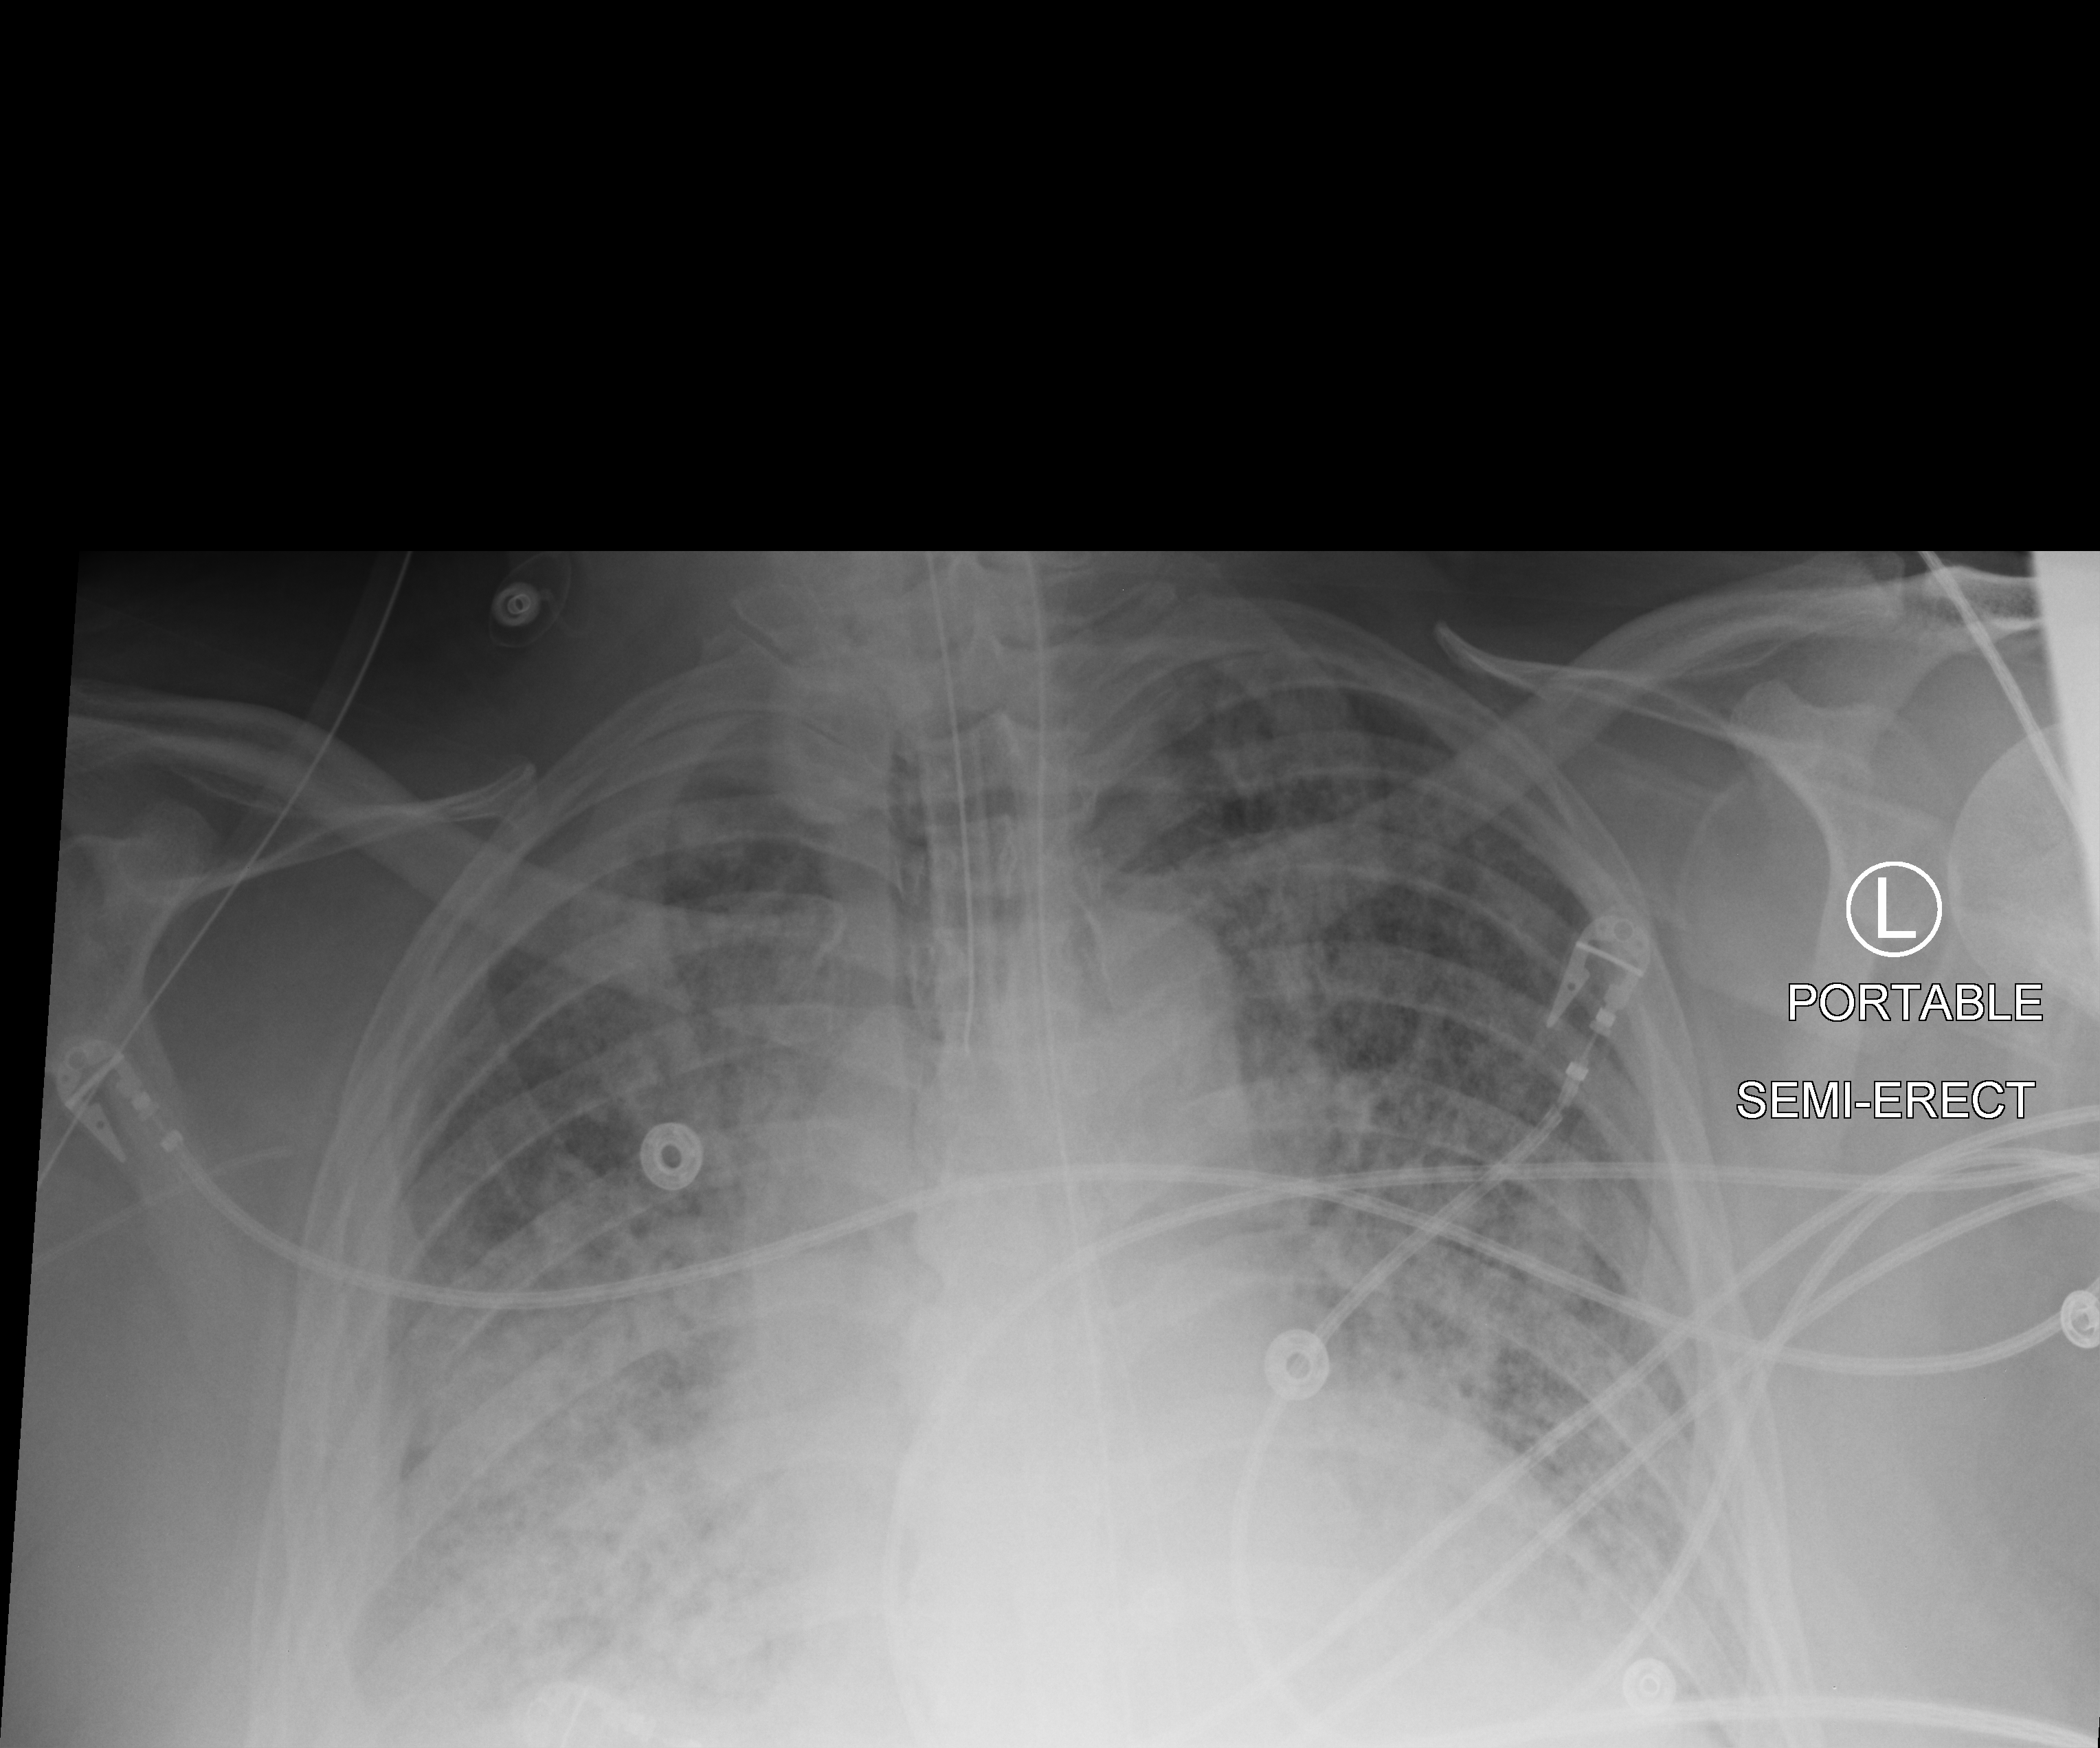
Portable chest radiograph; anteroposterior (AP) projection. Patient hospitalised with COVID-19; male, aged 60–74 years.
Hospital-stay facts (about this admission, not read from this image; timing relative to this image not recorded): chronic kidney disease (admission record): no.